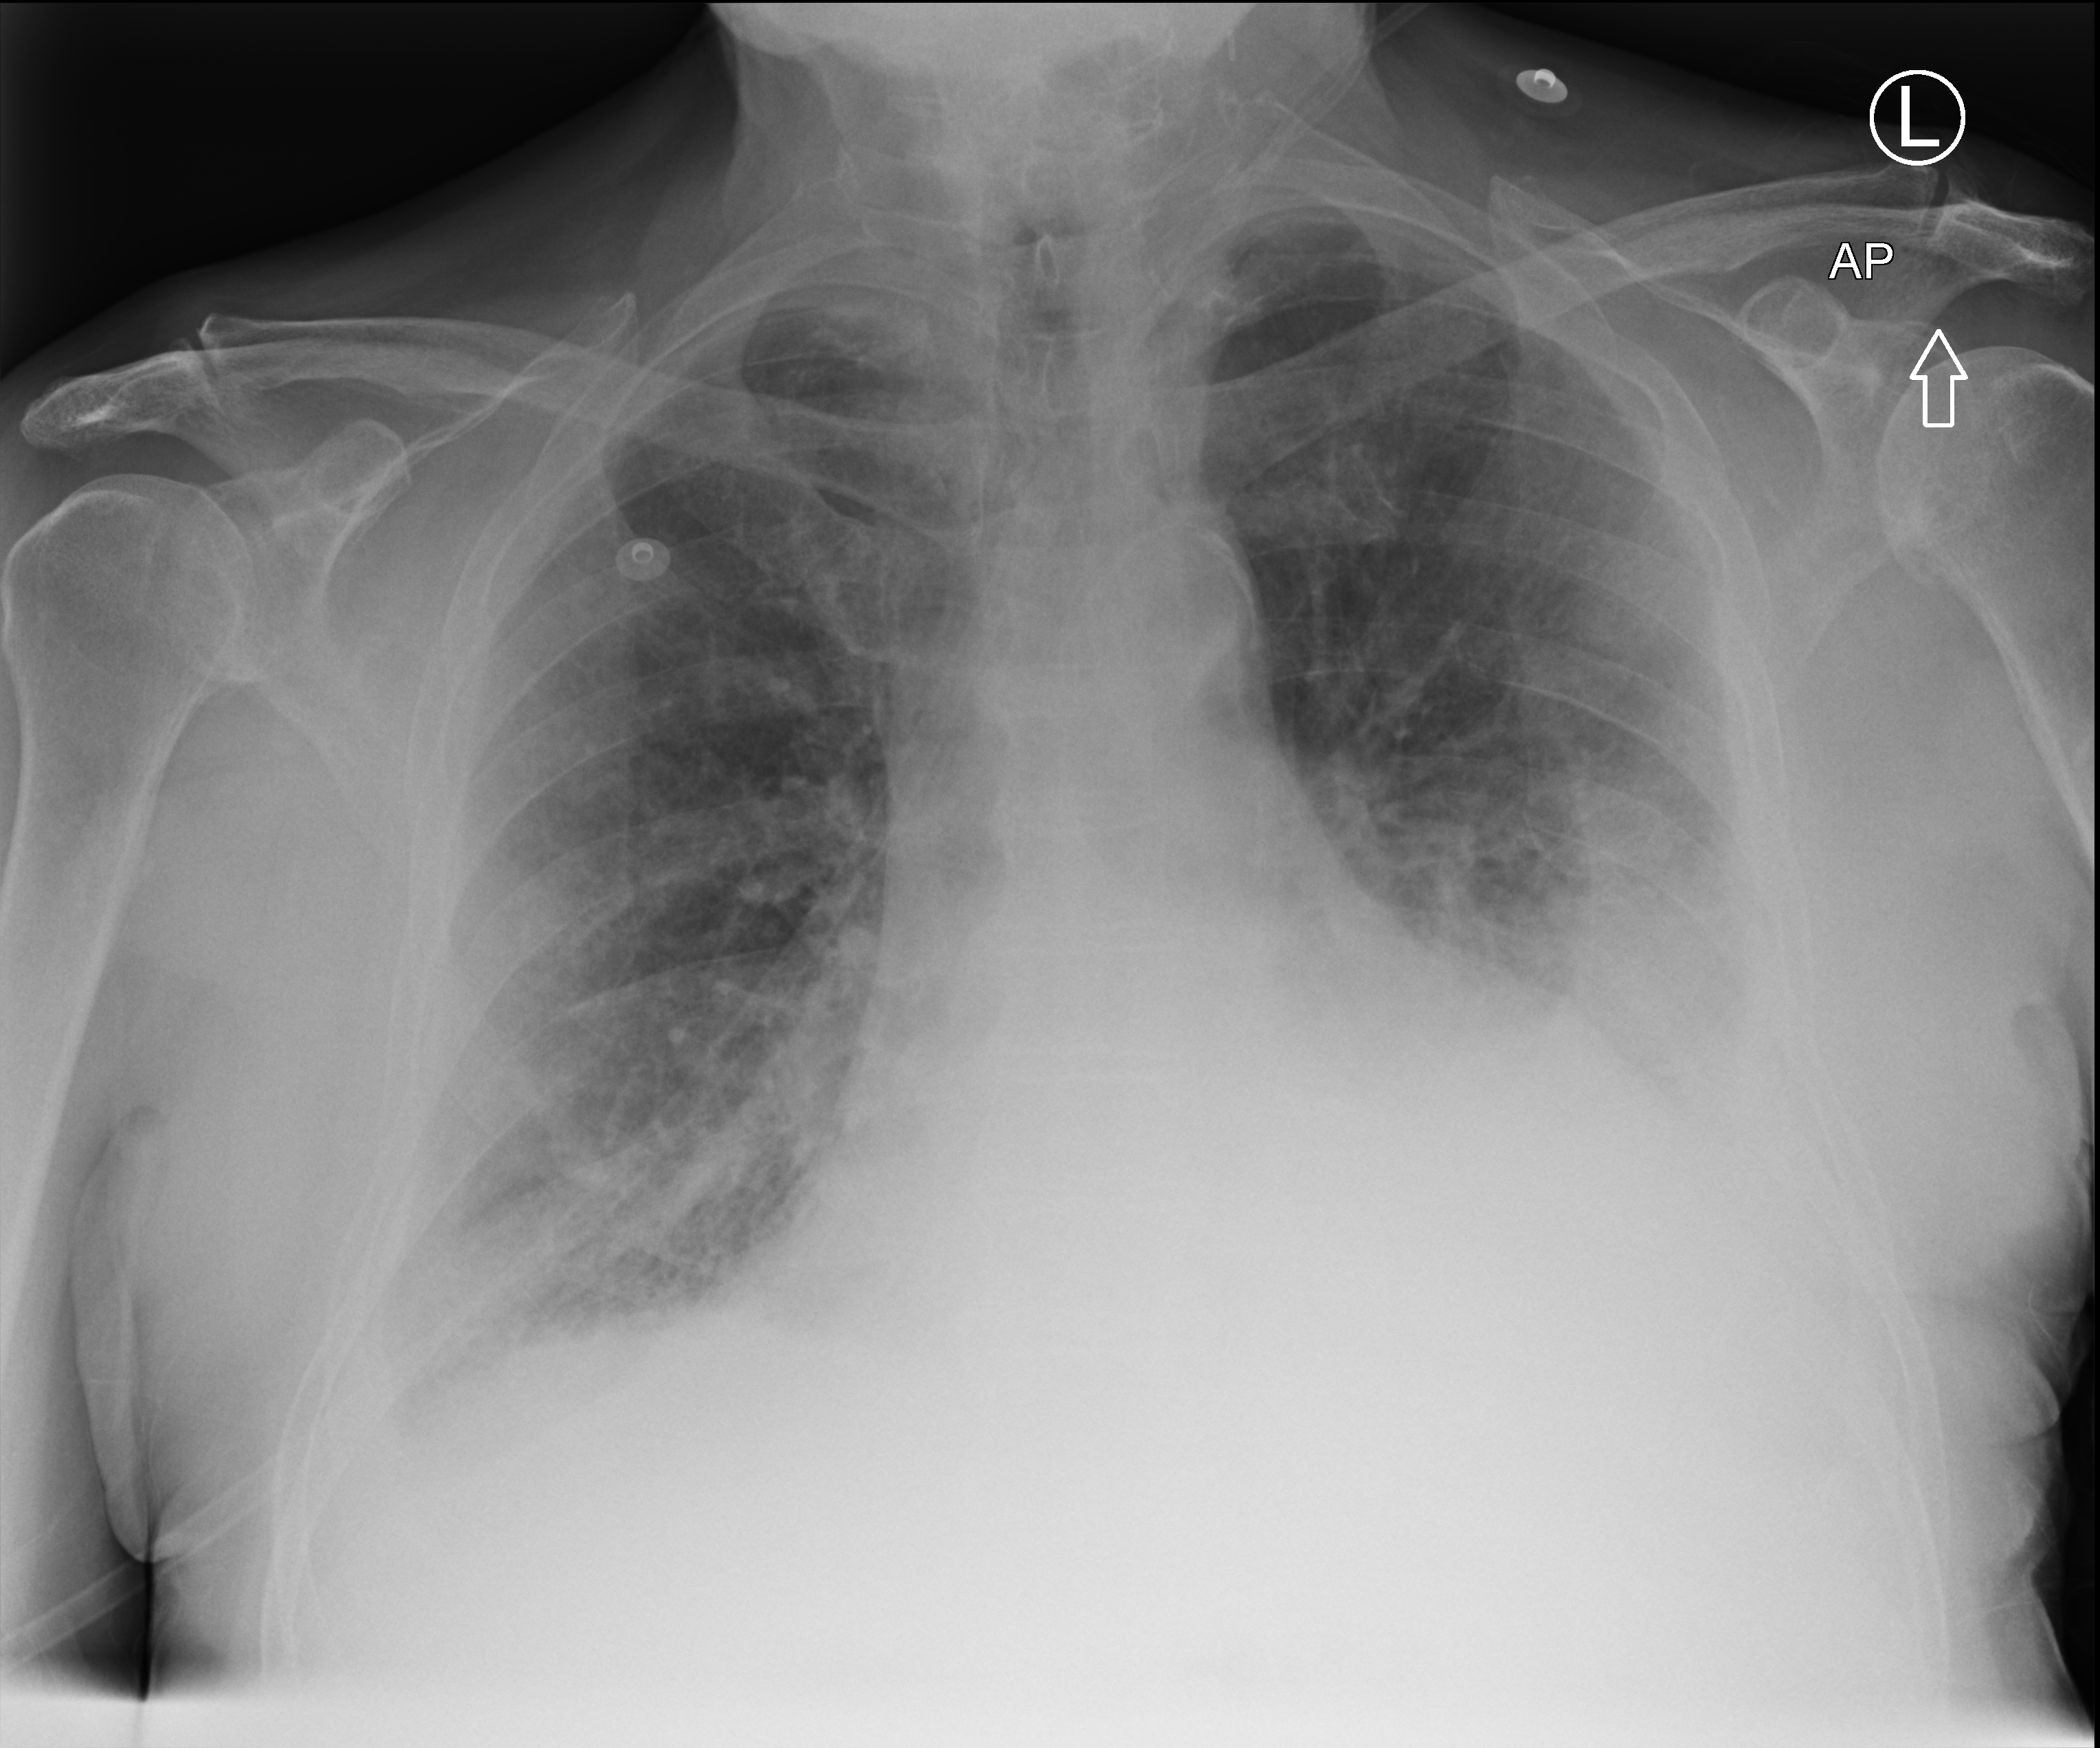
Chest radiograph (computed radiography), anteroposterior (AP) projection. Patient hospitalised with COVID-19; male, aged 75–90 years.
Admission-level facts for this patient (not findings on this image; timing relative to this image not recorded):
- admitted to intensive care during this hospital stay: yes